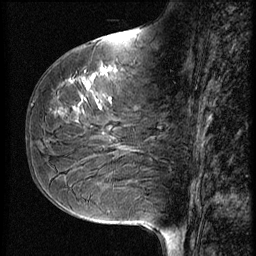
Breast MRI (dynamic contrast-enhanced), one sagittal slice; slice 26 of 56 in the series (ordered by position); 3 images stored at this slice position (order not interpretable as contrast timing); 1.5 T; TE 4.2 ms, TR 9 ms; 2.5 mm slice thickness; 256 × 256 image matrix. Female patient, age 51 years. From the clinical record (not read from this slice): setting: breast cancer imaged before/during neoadjuvant chemotherapy; receptor status: HR-positive, HER2-negative.
Annotated regions visible in this slice (semi-automatic segmentation, software-assisted and operator-edited):
- analysis volume of interest (the breast-tissue region the enhancement analysis was run in; not a lesion): bounding box <41,58,167,161> (left, top, right, bottom; pixels)
- tumour enhancement mask (voxels above the 140 % enhancement threshold inside the analysis volume of interest): <58,68,111,129>